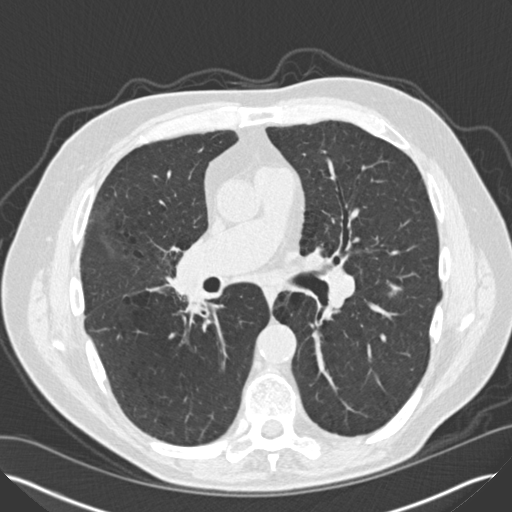
Axial slice from a low-dose chest CT screening exam, second screening round (one year after baseline), lung window (W 1500 / L -600 HU), 2 mm slice thickness, standard (soft-tissue) reconstruction kernel (B30f), 120 kVp, slice 73 of 149 in the series. Male, age 65 years at enrolment. Current smoker at enrolment.
Expert-annotated lung lesion, bounding box (x1, y1, x2, y2) in pixels: (370, 273, 416, 313). Reader record for this screening exam (exam-level; its link to the box is not recorded): non-calcified nodule or mass ≥4 mm, left lower lobe, 12 × 8 mm, smooth margins, soft tissue attenuation, pre-existing on the prior screen: yes; interval growth: yes. Official screen result: positive, other.